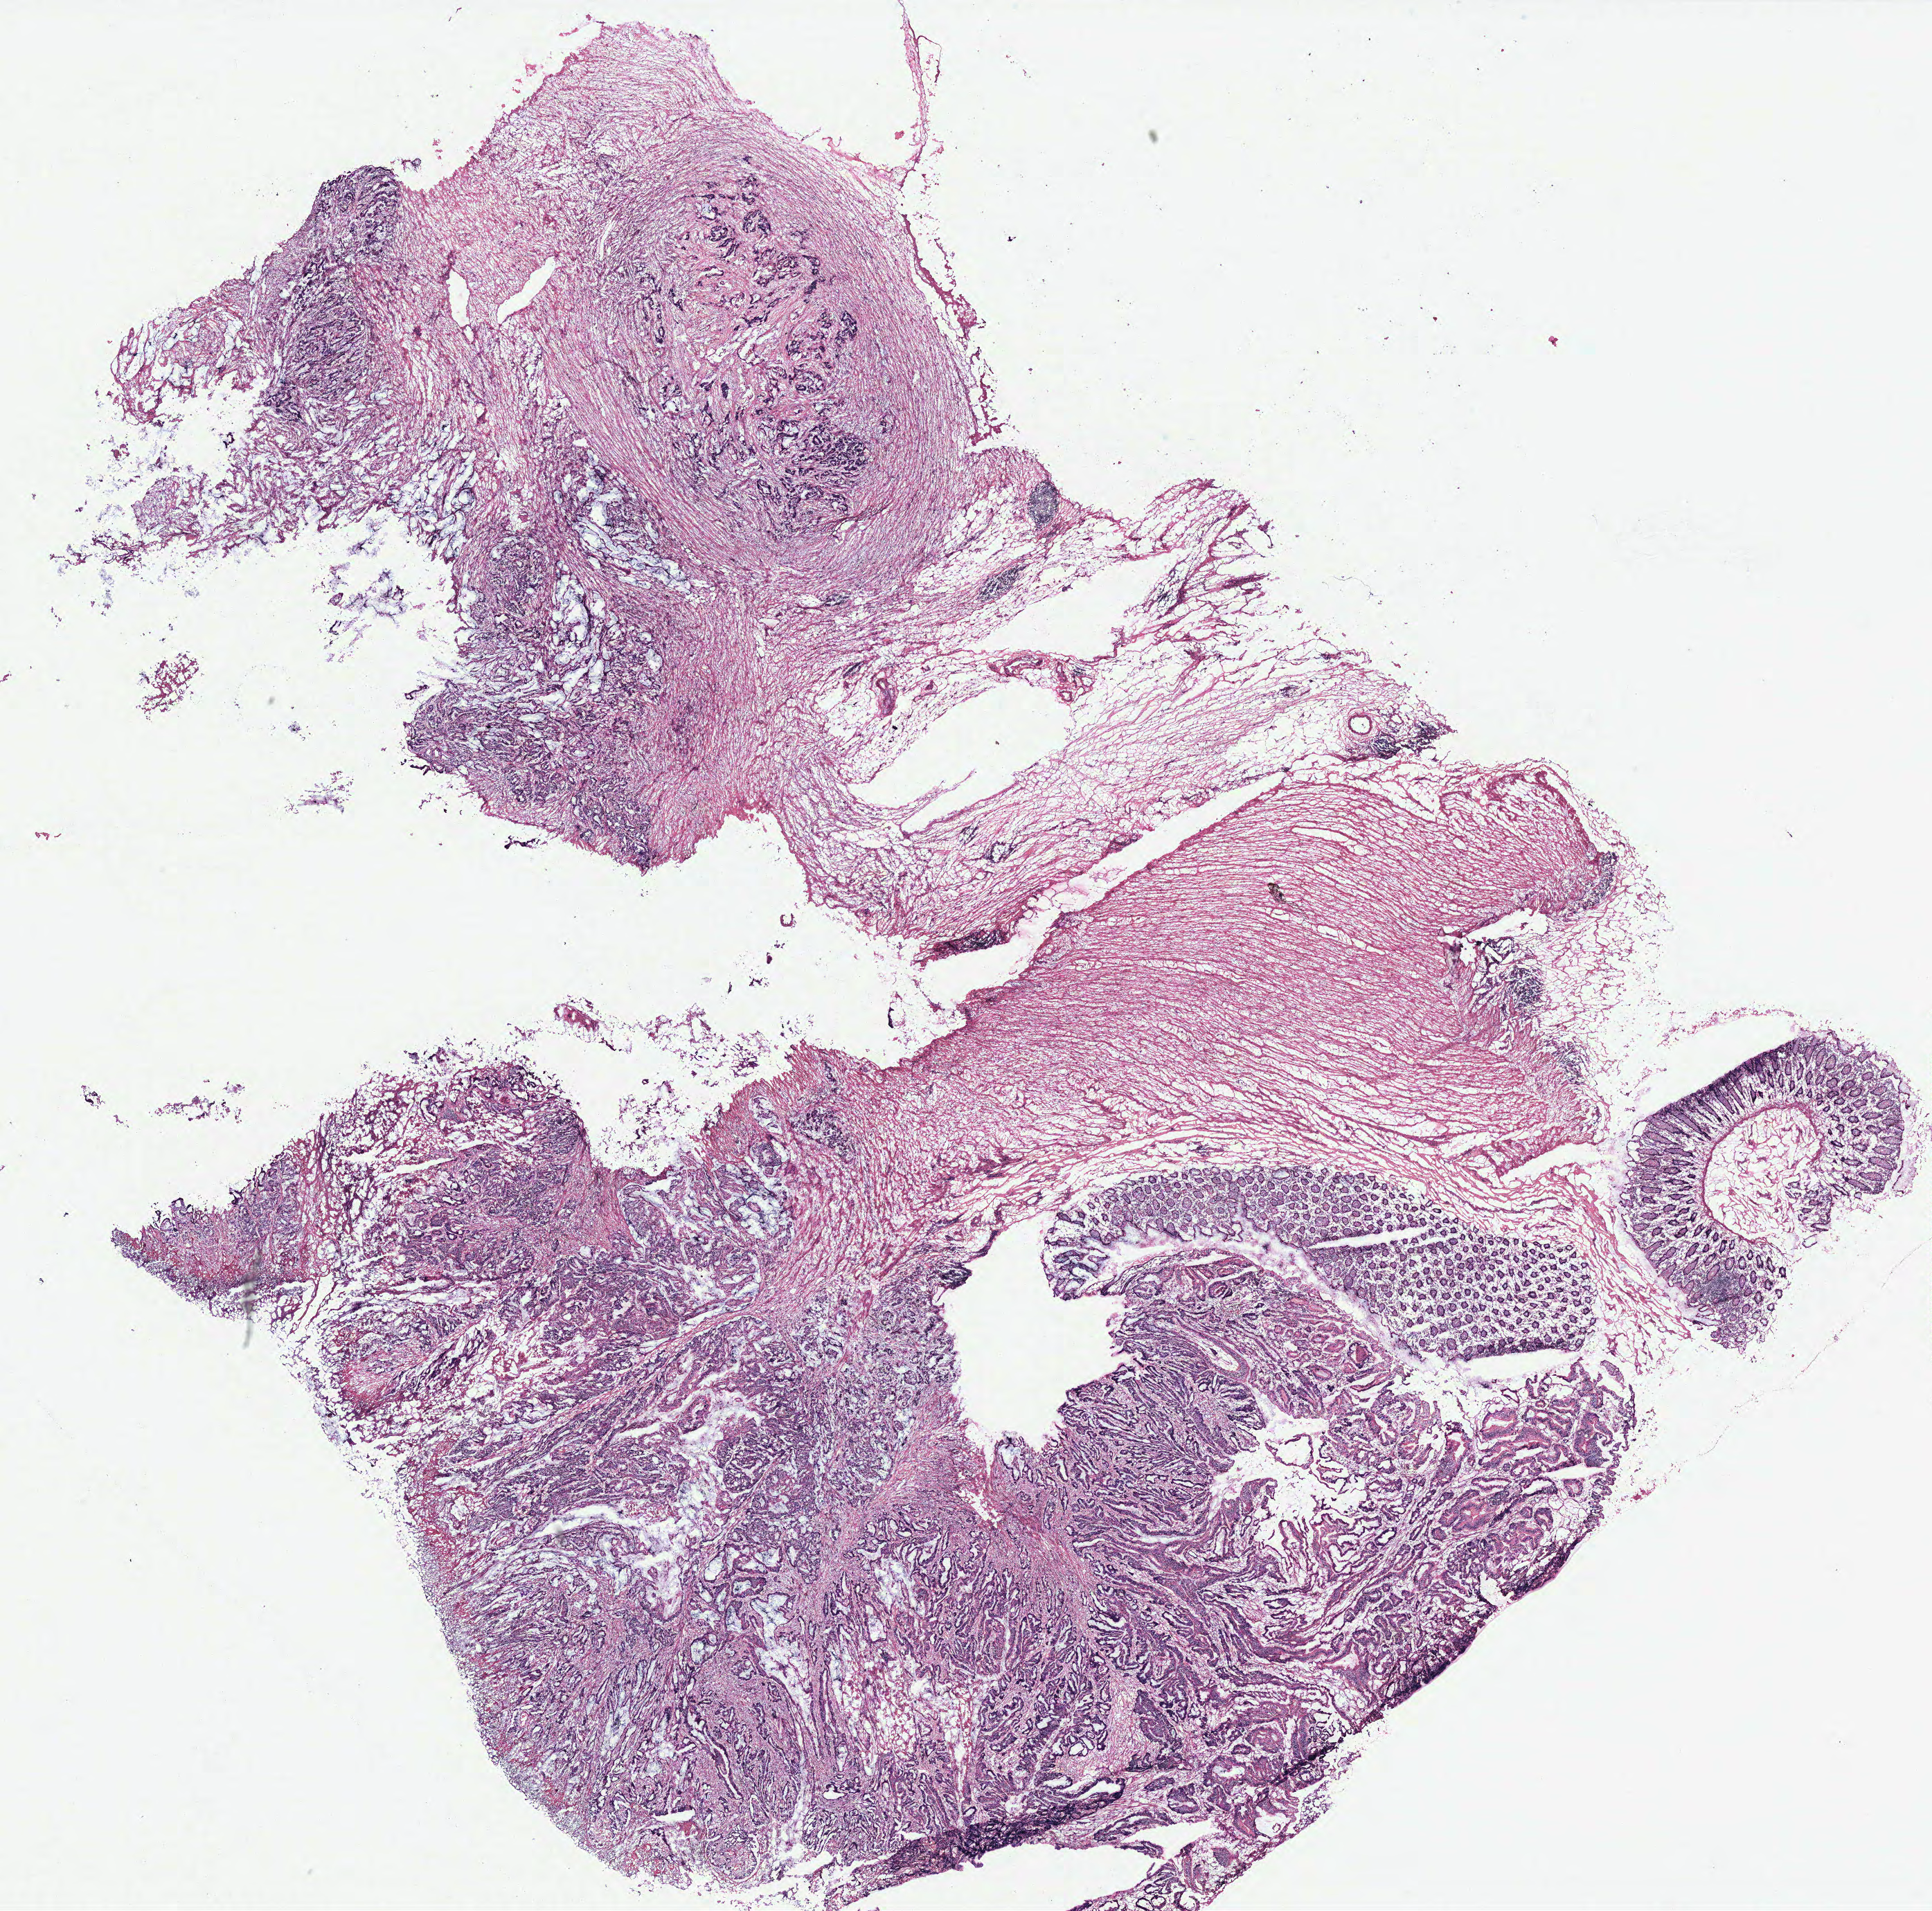
Digitized H&E tissue section (whole slide), whole scanned area (about 22.3 x 22.1 mm) shown as a low-resolution overview; colon, tissue type not recorded.
Patient diagnosis (cohort enrolment): colon cancer (colon).